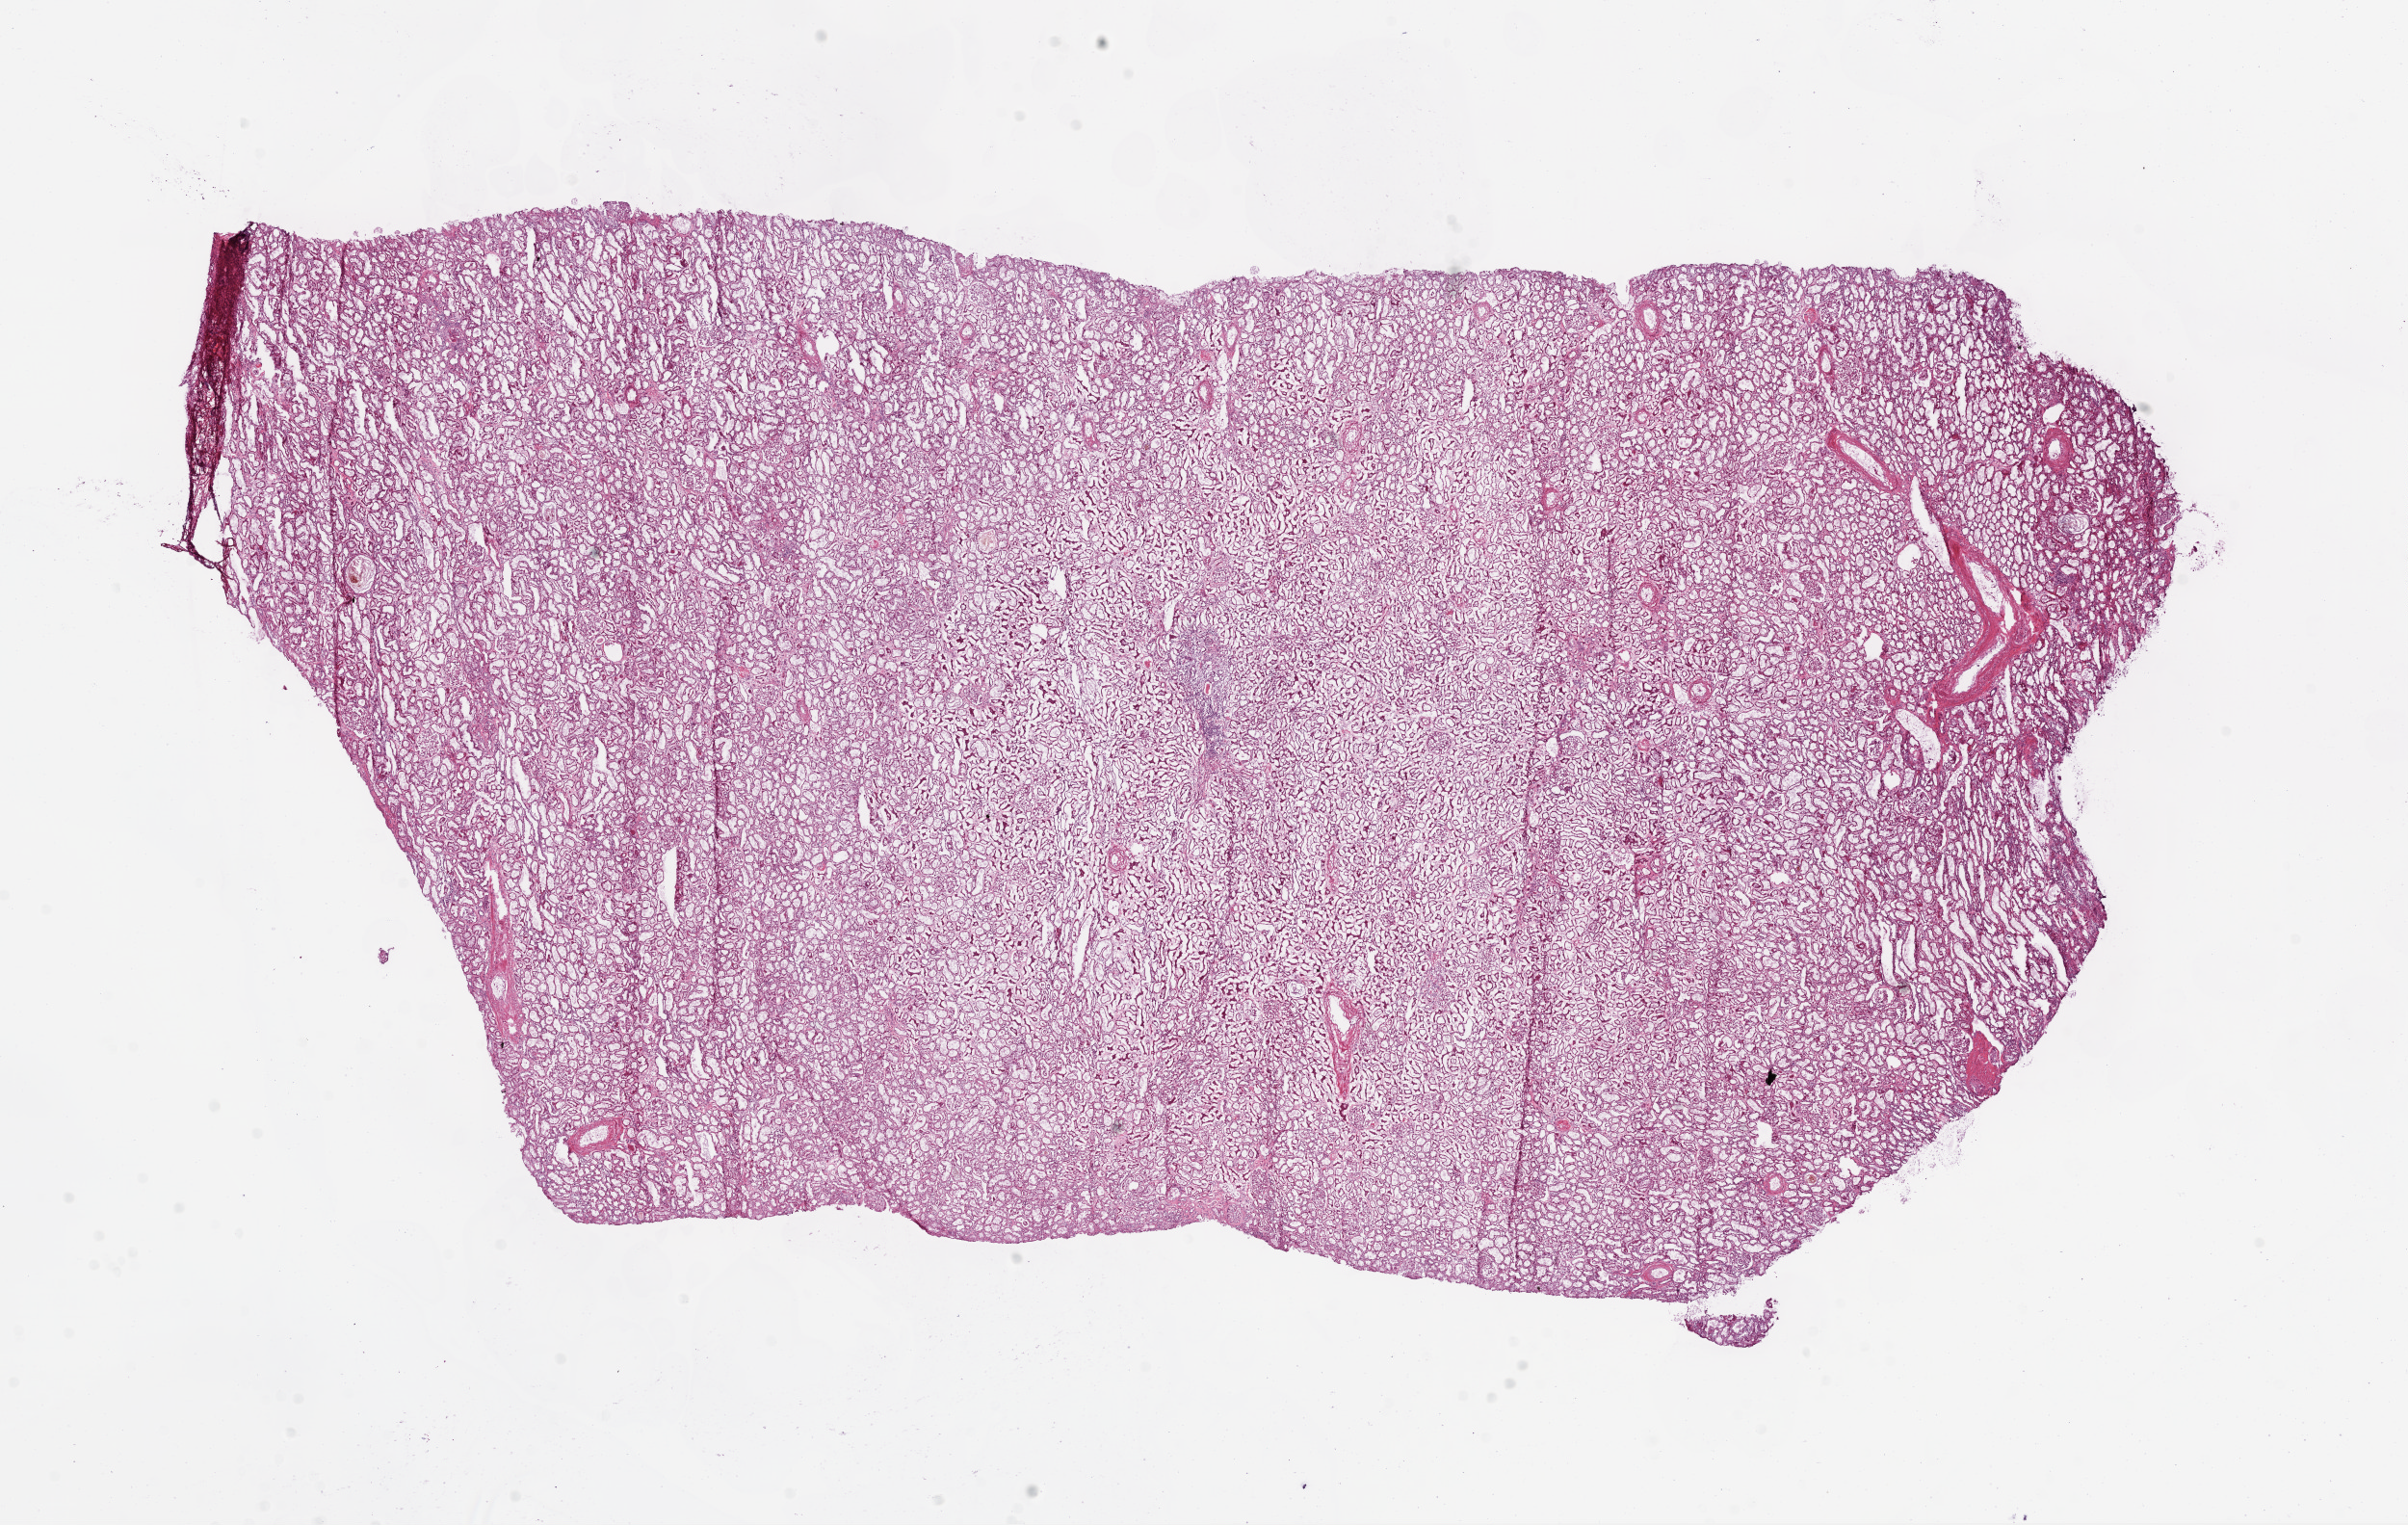
Whole-slide histology image, H&E-stained — shown as a low-resolution overview of the whole scanned area (about 20.1 x 12.7 mm, slide scanned at 20x), frozen section, sample: solid tissue normal (non-tumour tissue), kidney. Patient: male, age at initial diagnosis 69 years.
This section: solid tissue normal sample (biorepository sample class). Patient diagnosis: Clear cell adenocarcinoma, NOS.